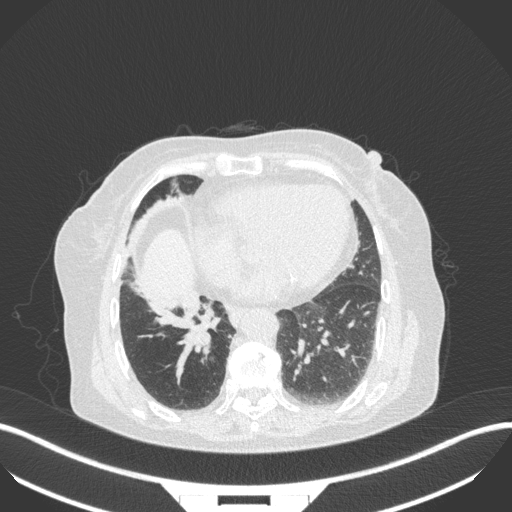
Chest CT, one axial slice. Slice 111 of 329 in the series (ordered by position). 120 kVp. Lung window (W 1500 / L -600 HU). 1 mm slice thickness. 512 × 512 image matrix, field of view 400 × 400 mm. Patient: female, 75 years. Case-level facts recorded for this patient, not image findings: clinical TNM (as recorded): T1b N0 M1a; histopathological grade: G1.
Outlined on this slice (bounding box drawn by a radiologist):
- lung tumour (recorded histology: squamous cell carcinoma): box from (x=181, y=303) to (x=218, y=356) px